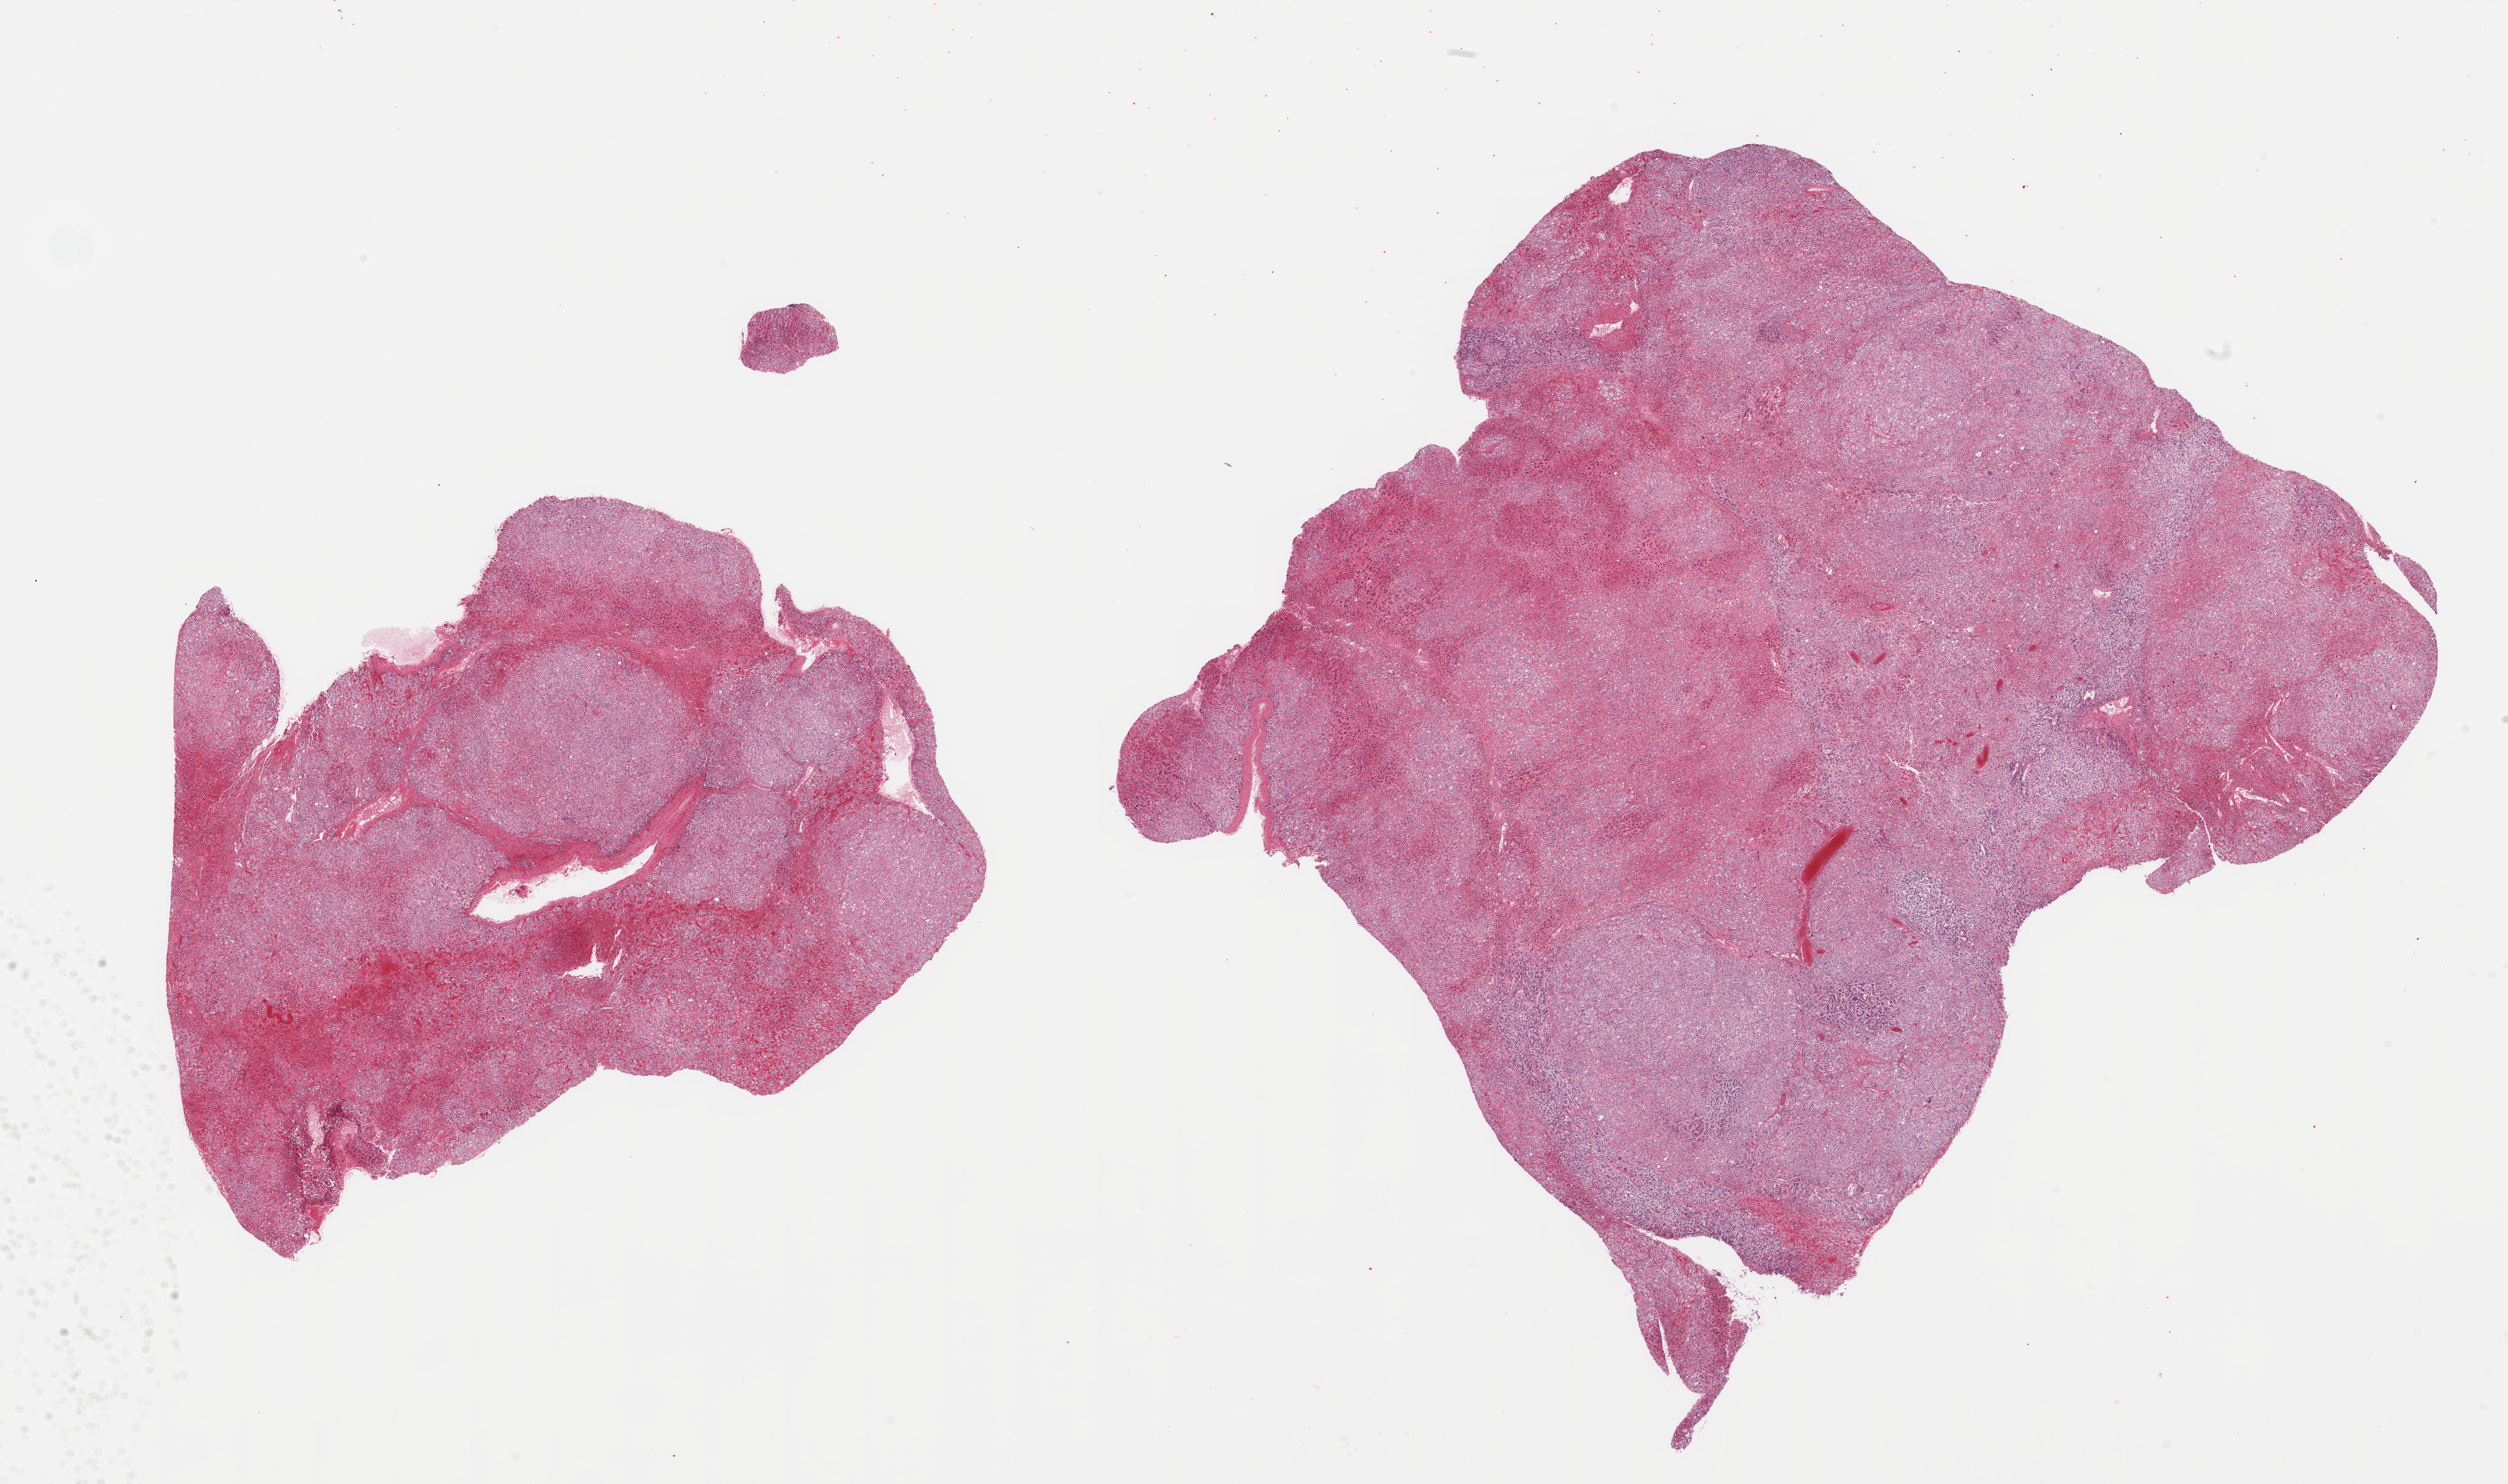
Haematoxylin and eosin whole-slide image, brightfield — low-resolution overview of the scanned area, about 31.5 x 18.6 mm (from a 20x scan); PAXgene-fixed paraffin-embedded (PFPE) section; target tissue: adrenal gland; donor tissue sample. Donor sex: female.
Pathologist's review note for this sample: 2 pieces; well dissected, no external fat.